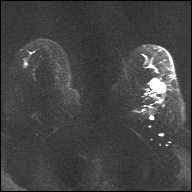
Breast MRI, one axial slice; slice 23 of 32 in the series (ordered by position); diffusion-weighted series; image 2 of 4 stored at this slice position (different b-values; order by instance number); 1.5 T; 4 mm slice thickness; 192 × 192 image matrix, field of view 360 × 360 mm. Female patient.
Structures marked on this image (manually delineated by an expert):
- tumour on diffusion-weighted imaging: box from (x=151, y=80) to (x=164, y=89) px